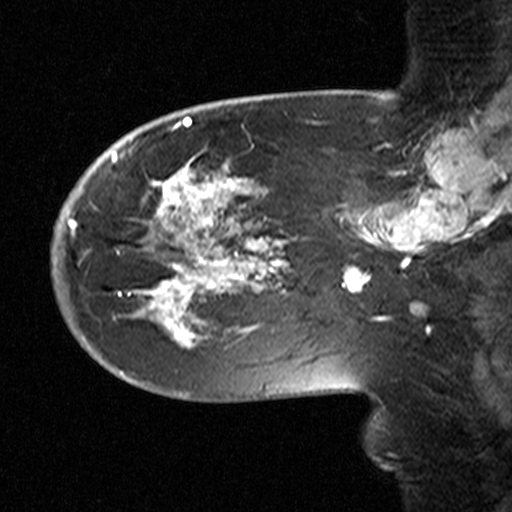
Breast MRI (dynamic contrast-enhanced), one sagittal slice. Position 14 of 44 along the scan axis. Dynamic contrast-enhanced study with each time point stored as its own series, time point 2 of 3 at this slice position (early post-contrast, ordered by acquisition time). 1.5 T. TE 4.5 ms, TR 11 ms. 3.27 mm slice thickness. 512 × 512 image matrix, field of view 200 × 200 mm. Female patient, age 53 years. From the clinical record (not read from this slice): setting: breast cancer imaged before/during neoadjuvant chemotherapy; receptor status: HR-positive, HER2-negative.
Annotated regions visible in this slice (semi-automatically segmented with operator editing):
- analysis volume of interest (the breast-tissue region the enhancement analysis was run in; not a lesion): box from (x=58, y=154) to (x=311, y=367) px
- tumour enhancement mask (voxels above the 90 % enhancement threshold inside the analysis volume of interest): (x=68, y=160)–(x=296, y=345)